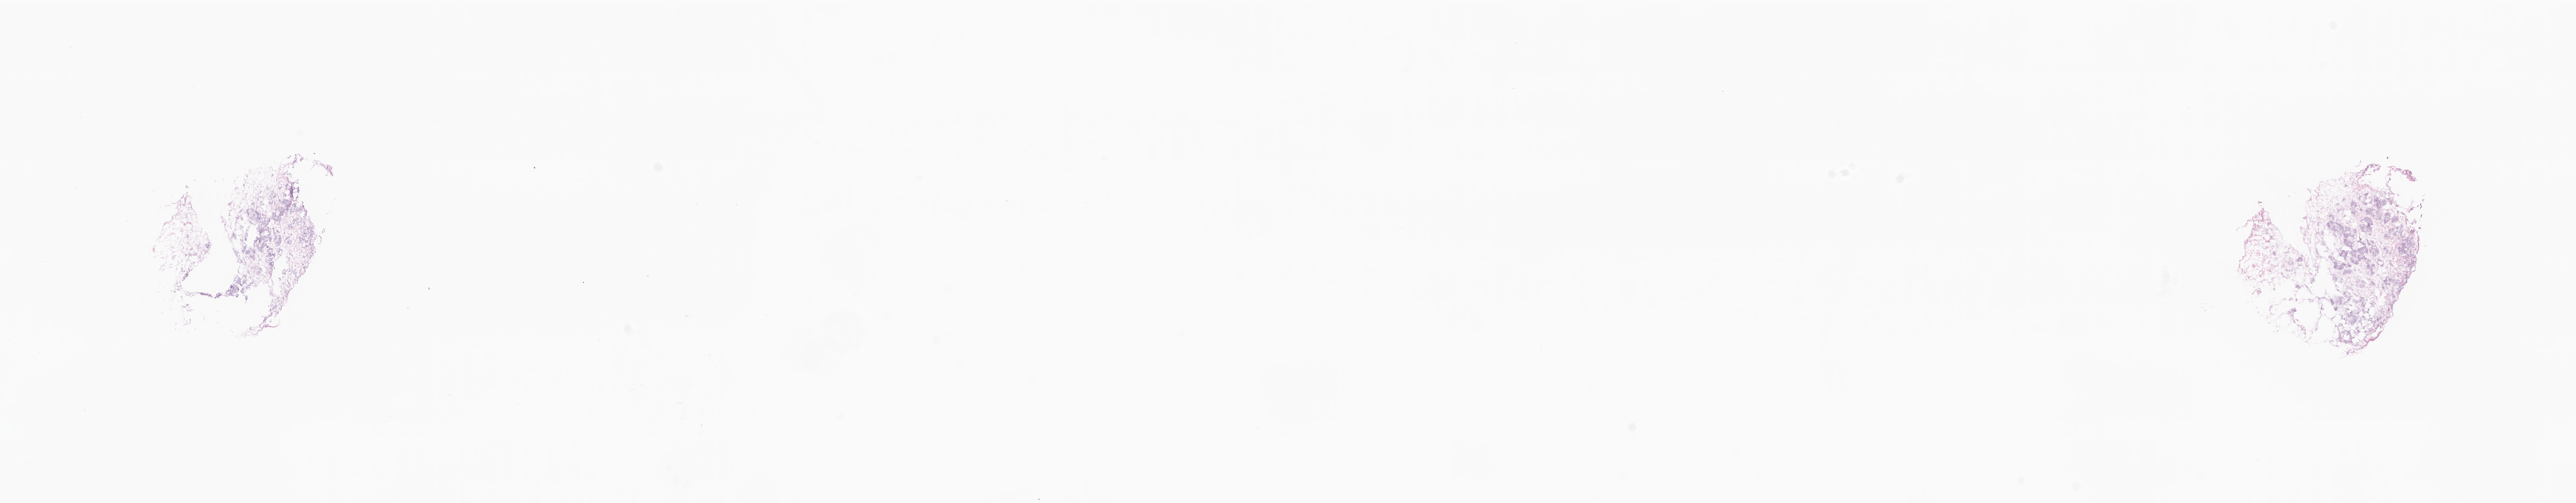
Whole-slide image, haematoxylin and eosin stain, whole scanned area (about 31.5 x 6.2 mm) shown as a low-resolution overview, frozen section (tissue freezing medium), primary tumor, anatomic site: breast (left). Patient: female, age at initial diagnosis 82 years. Composition of this section per pathologist review: tumor cells 80%, tumor nuclei 80%, stromal cells 0%, necrosis 0%, normal cells 20%. Inflammatory infiltration, as recorded: lymphocyte infiltration 0%, monocyte infiltration 0%, neutrophil infiltration 0%.
Diagnosis: Infiltrating duct carcinoma, NOS.